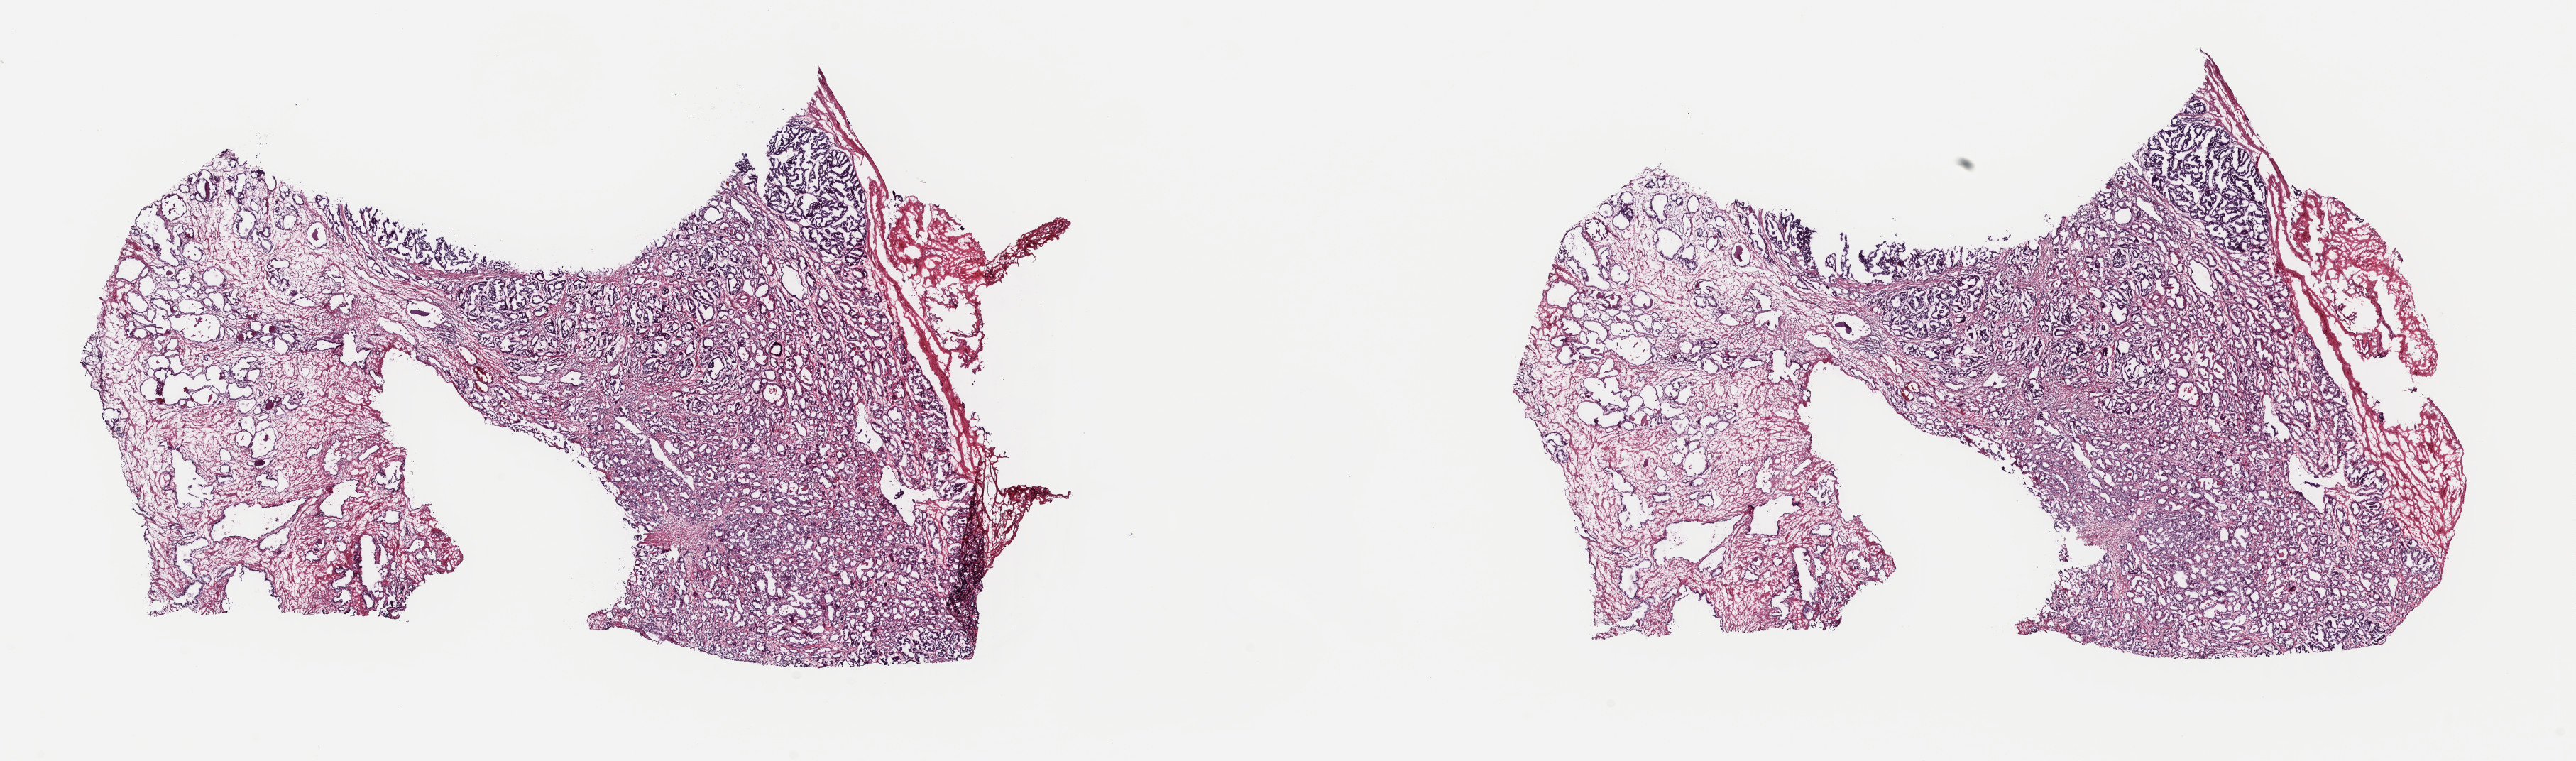
Whole-slide histology image, H&E — whole scanned area (about 28.6 x 8.5 mm, from a 40x scan) shown as a low-resolution overview. Frozen section from the top of the tissue portion. Primary tumour sample from the prostate. Patient: male, age at initial diagnosis 64 years. Gleason score: 7 (3+4). Pathologist review of this section (percent, as recorded): tumour cells 45%, tumour nuclei 70%, normal cells 14%, stromal cells 40%, necrosis 1%. Inflammatory infiltration, as recorded: lymphocyte infiltration 4%, monocyte infiltration 0%, neutrophil infiltration 0%.
Pathologic diagnosis: Adenocarcinoma, NOS (prostate gland).